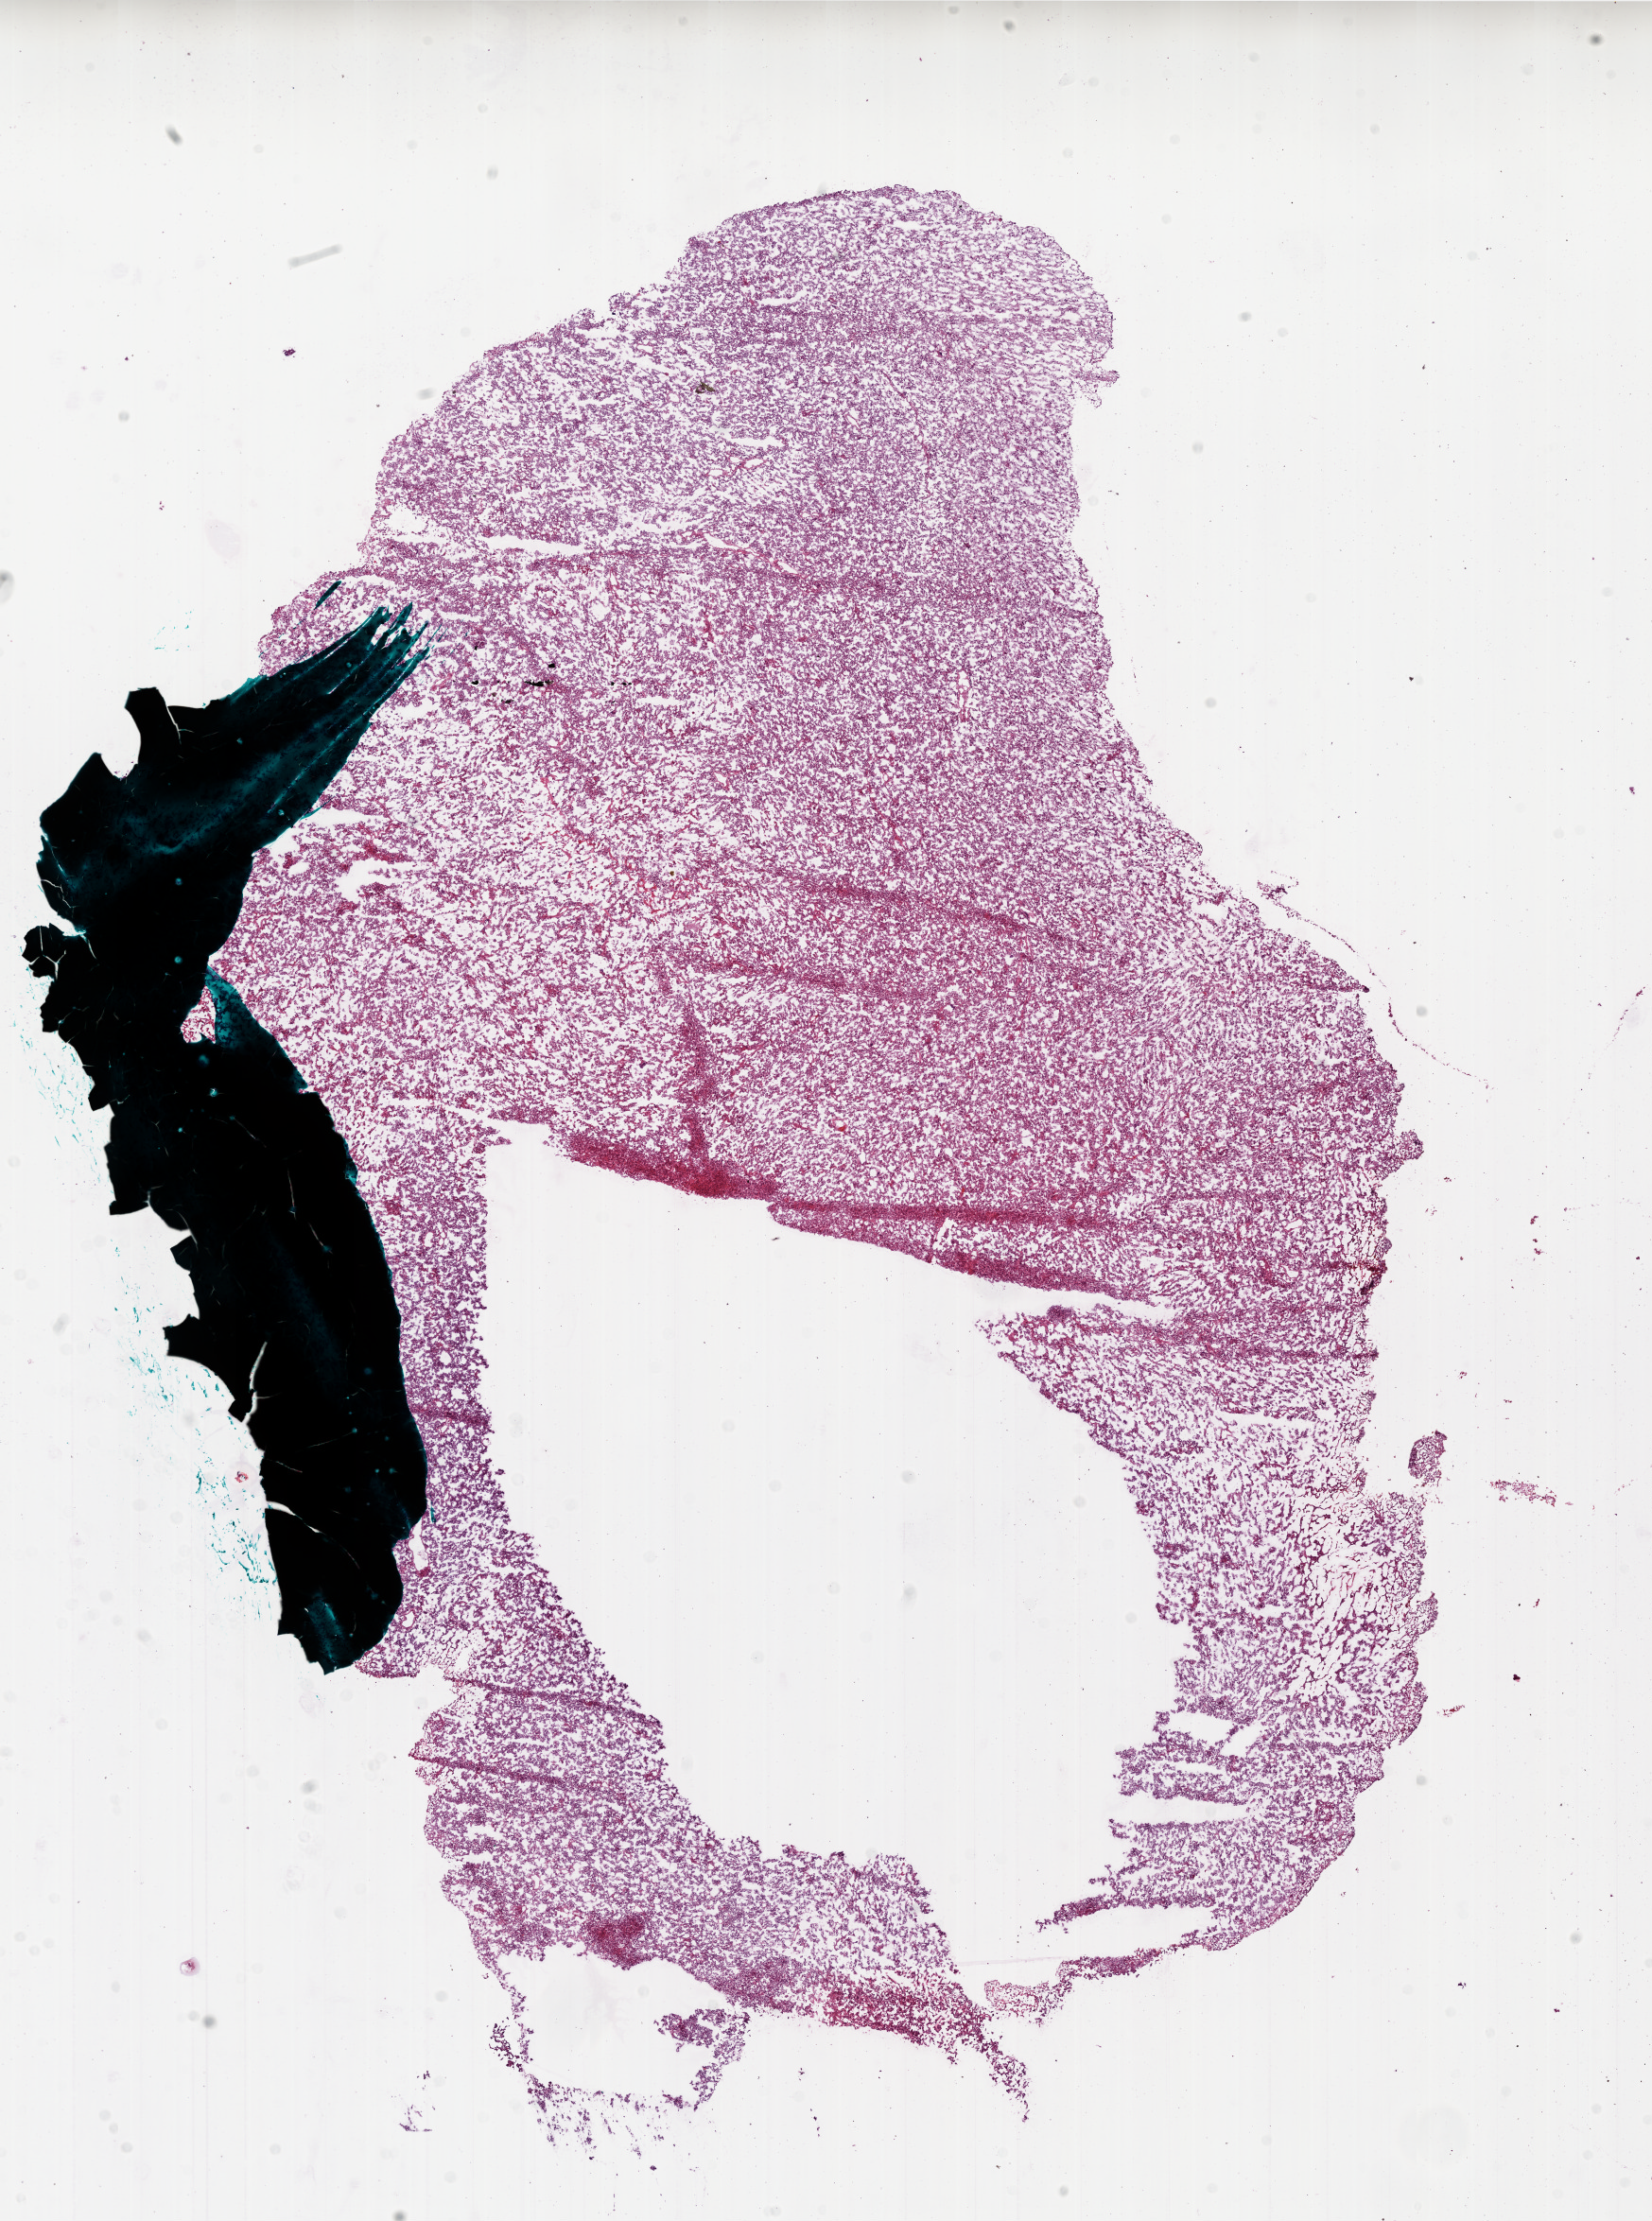
H&E-stained whole-slide image, shown as a low-resolution overview of the whole scanned area (about 14.0 x 18.8 mm); frozen section from the bottom of the tissue portion; brain, primary tumour sample. Male, age 41 years at initial diagnosis. Composition of this section per pathologist review: tumour cells 100%, tumour nuclei 100%, normal cells 0%, stromal cells 0%, necrosis 0%. Infiltration values recorded for this section: lymphocyte infiltration 0%.
* diagnosis: Glioblastoma